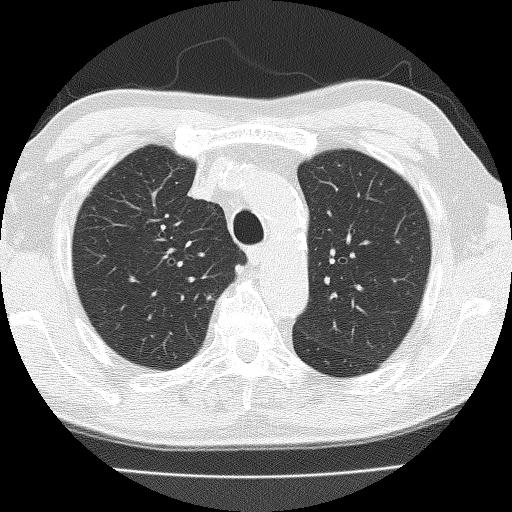
Chest CT (low-dose screening protocol), one axial image. Second screening round (one year after baseline). Lung window (W 1500 / L -600 HU). Slice 39 of 159 in the series. 512 × 512 image matrix, field of view 322 × 322 mm. Male, age 72 years at enrolment. Current smoker at enrolment.
Expert reader's lesion annotation, bounding box [x1, y1, x2, y2] px = [187, 279, 229, 318]. No non-calcified nodule or mass ≥4 mm was recorded by the screening reader at this exam. Official screen result: negative screen, significant abnormalities not suspicious for lung cancer. Participant outcome: lung cancer diagnosed 396 days after this screen — squamous cell carcinoma, NOS, right upper lobe, moderately differentiated (G2), stage IIA (AJCC 6th edition), 25 mm at pathology.